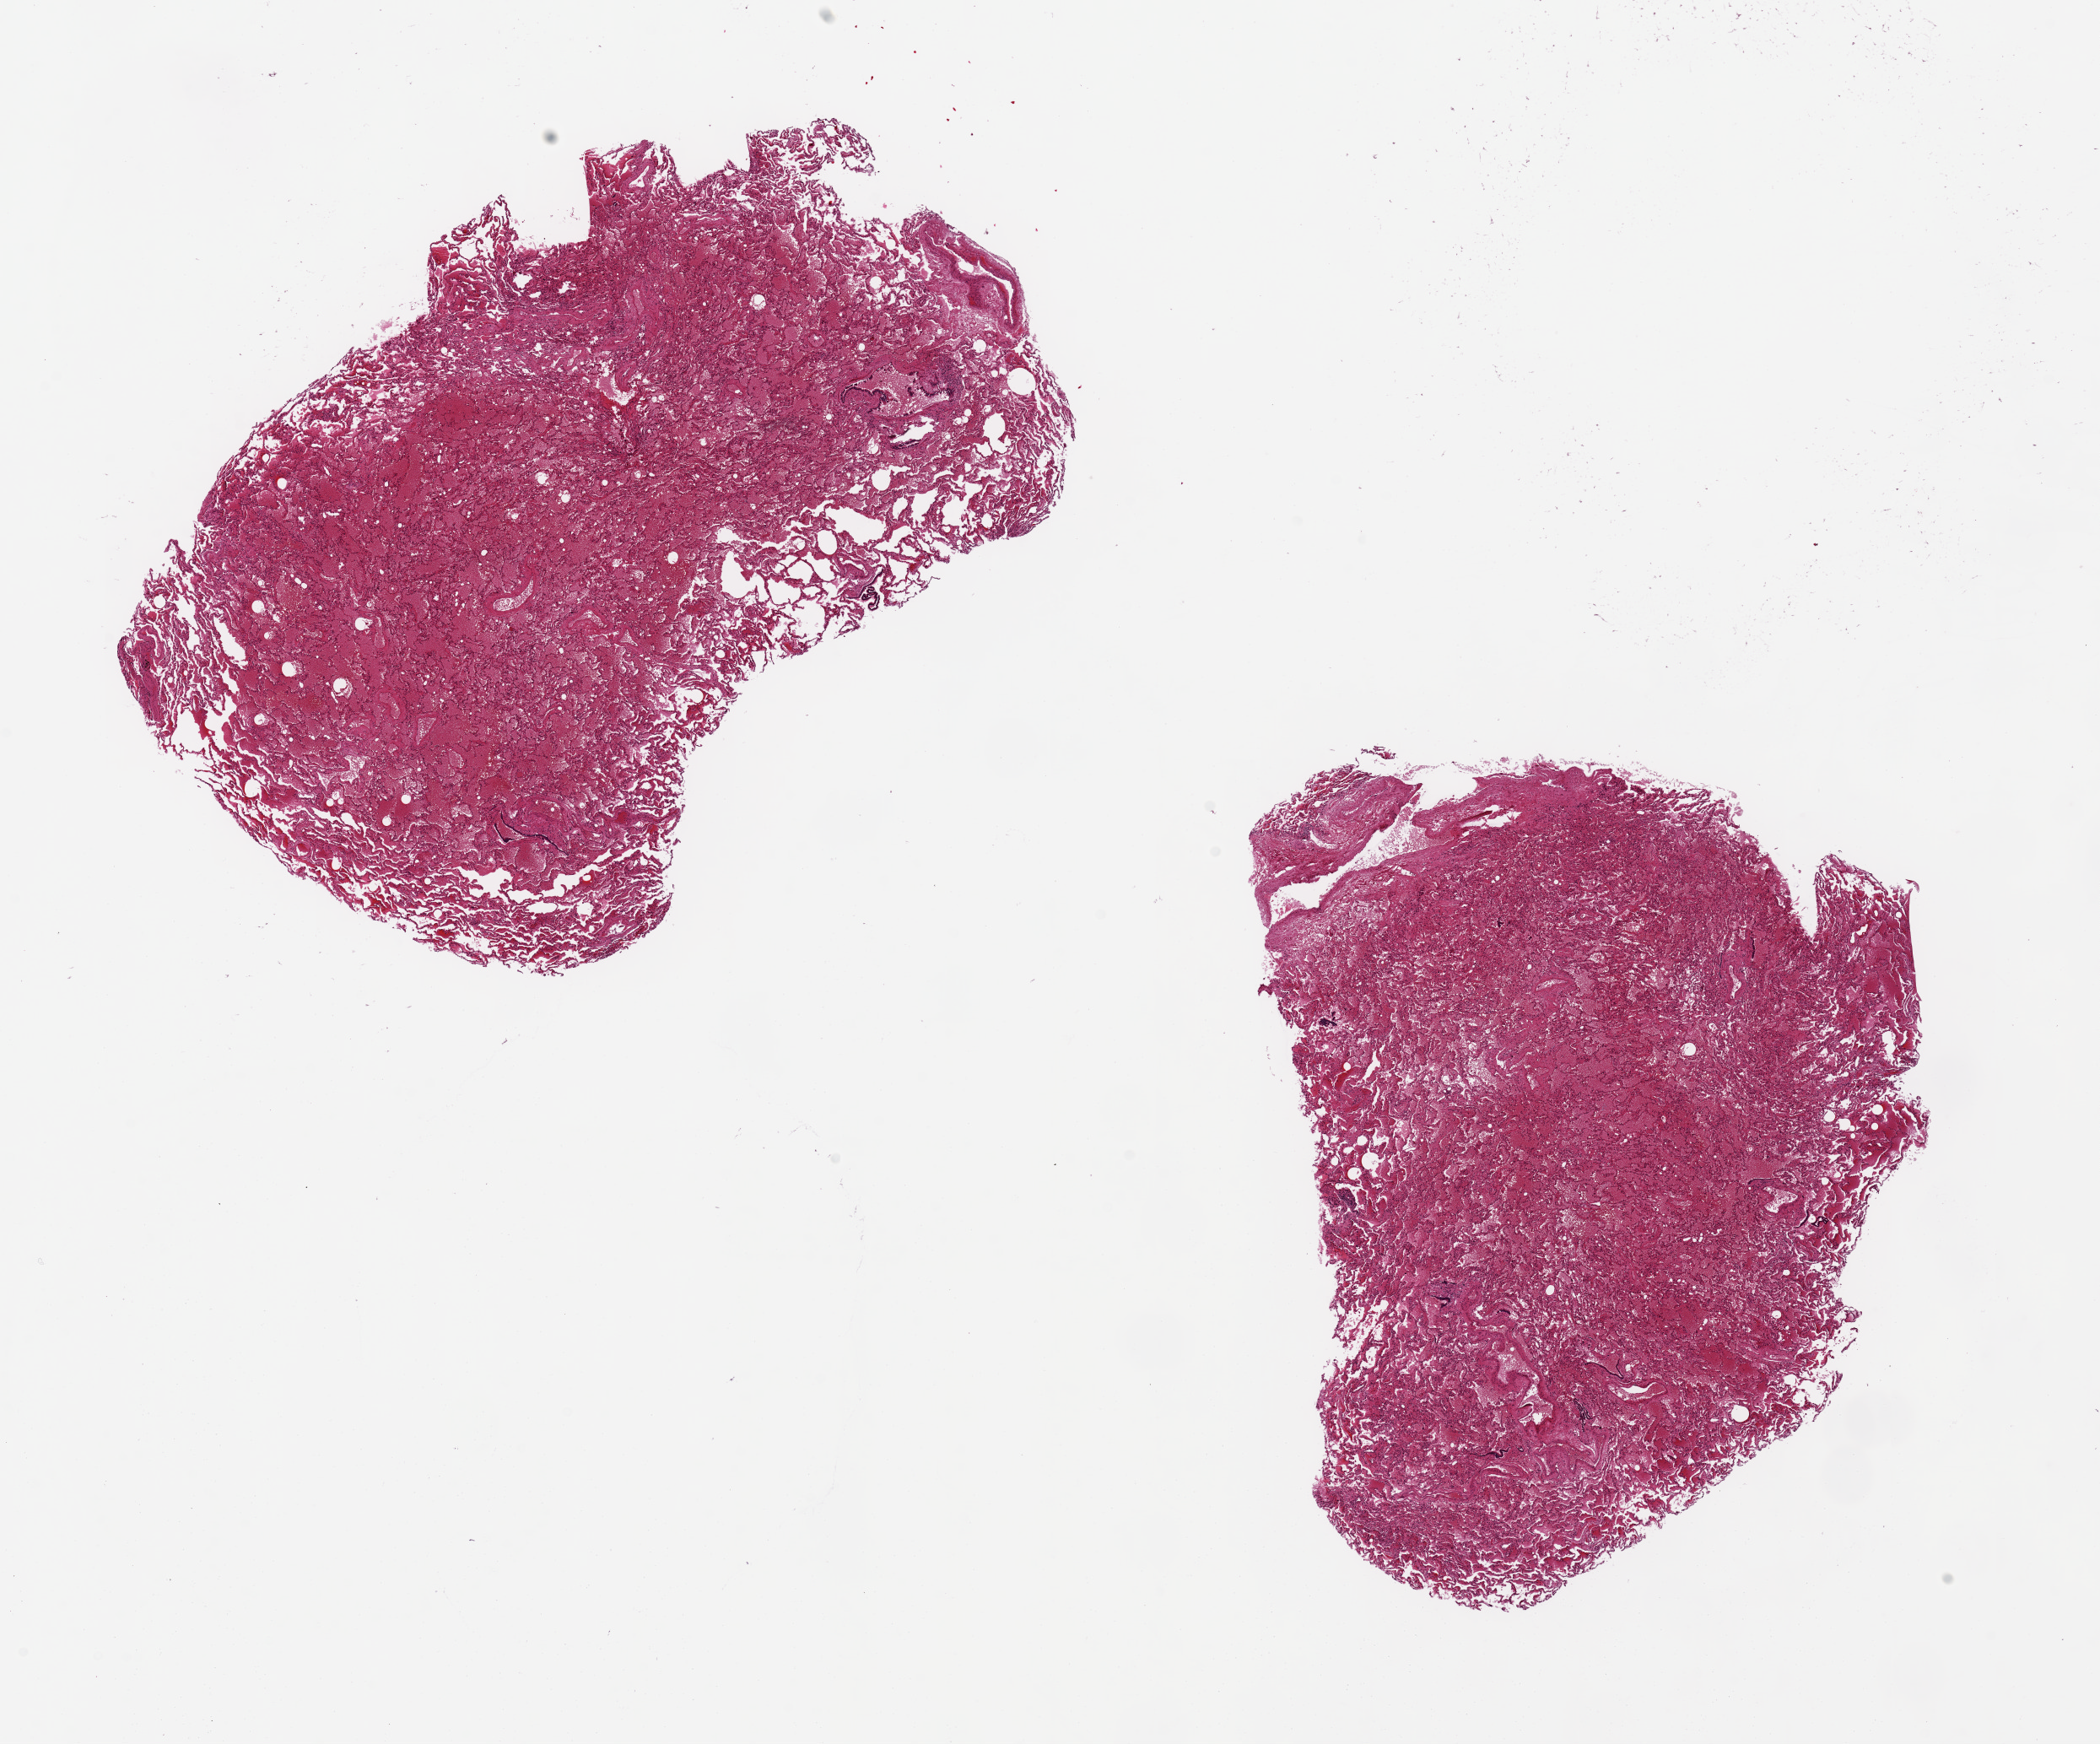
Whole-slide image, haematoxylin and eosin stain, brightfield, whole scanned area (about 19.7 x 16.4 mm, acquisition: 20x scan) shown as a low-resolution overview, PAXgene-fixed paraffin-embedded (PFPE) section, section of lung (target tissue), donor tissue sample.
Reviewer comment on this tissue sample: 2 aliquots, ~8x5mm. Severe diffuse alveolar congestion/edema.